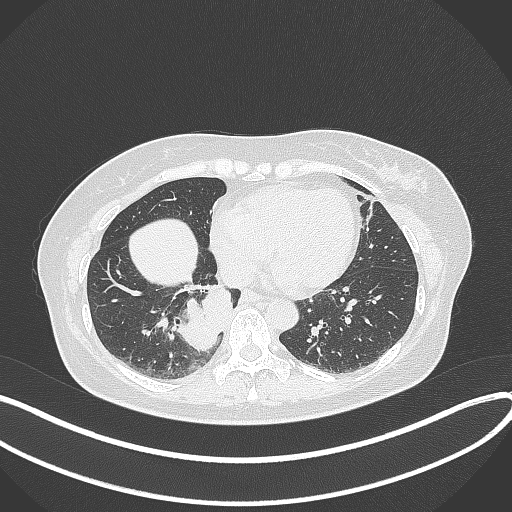
Chest CT, one axial slice; position 118 of 331 along the scan axis; 120 kVp; lung window (W 1500 / L -600 HU); 1 mm slice thickness; 512 × 512 image matrix. Female patient, age 54 years. From the clinical record (not read from this slice): clinical TNM (as recorded): T4 N0 M0.
Annotated regions visible in this slice (bounding box drawn by a radiologist):
- lung tumour (recorded histology: adenocarcinoma): bounding box [x1, y1, x2, y2] px = [163, 275, 233, 350]